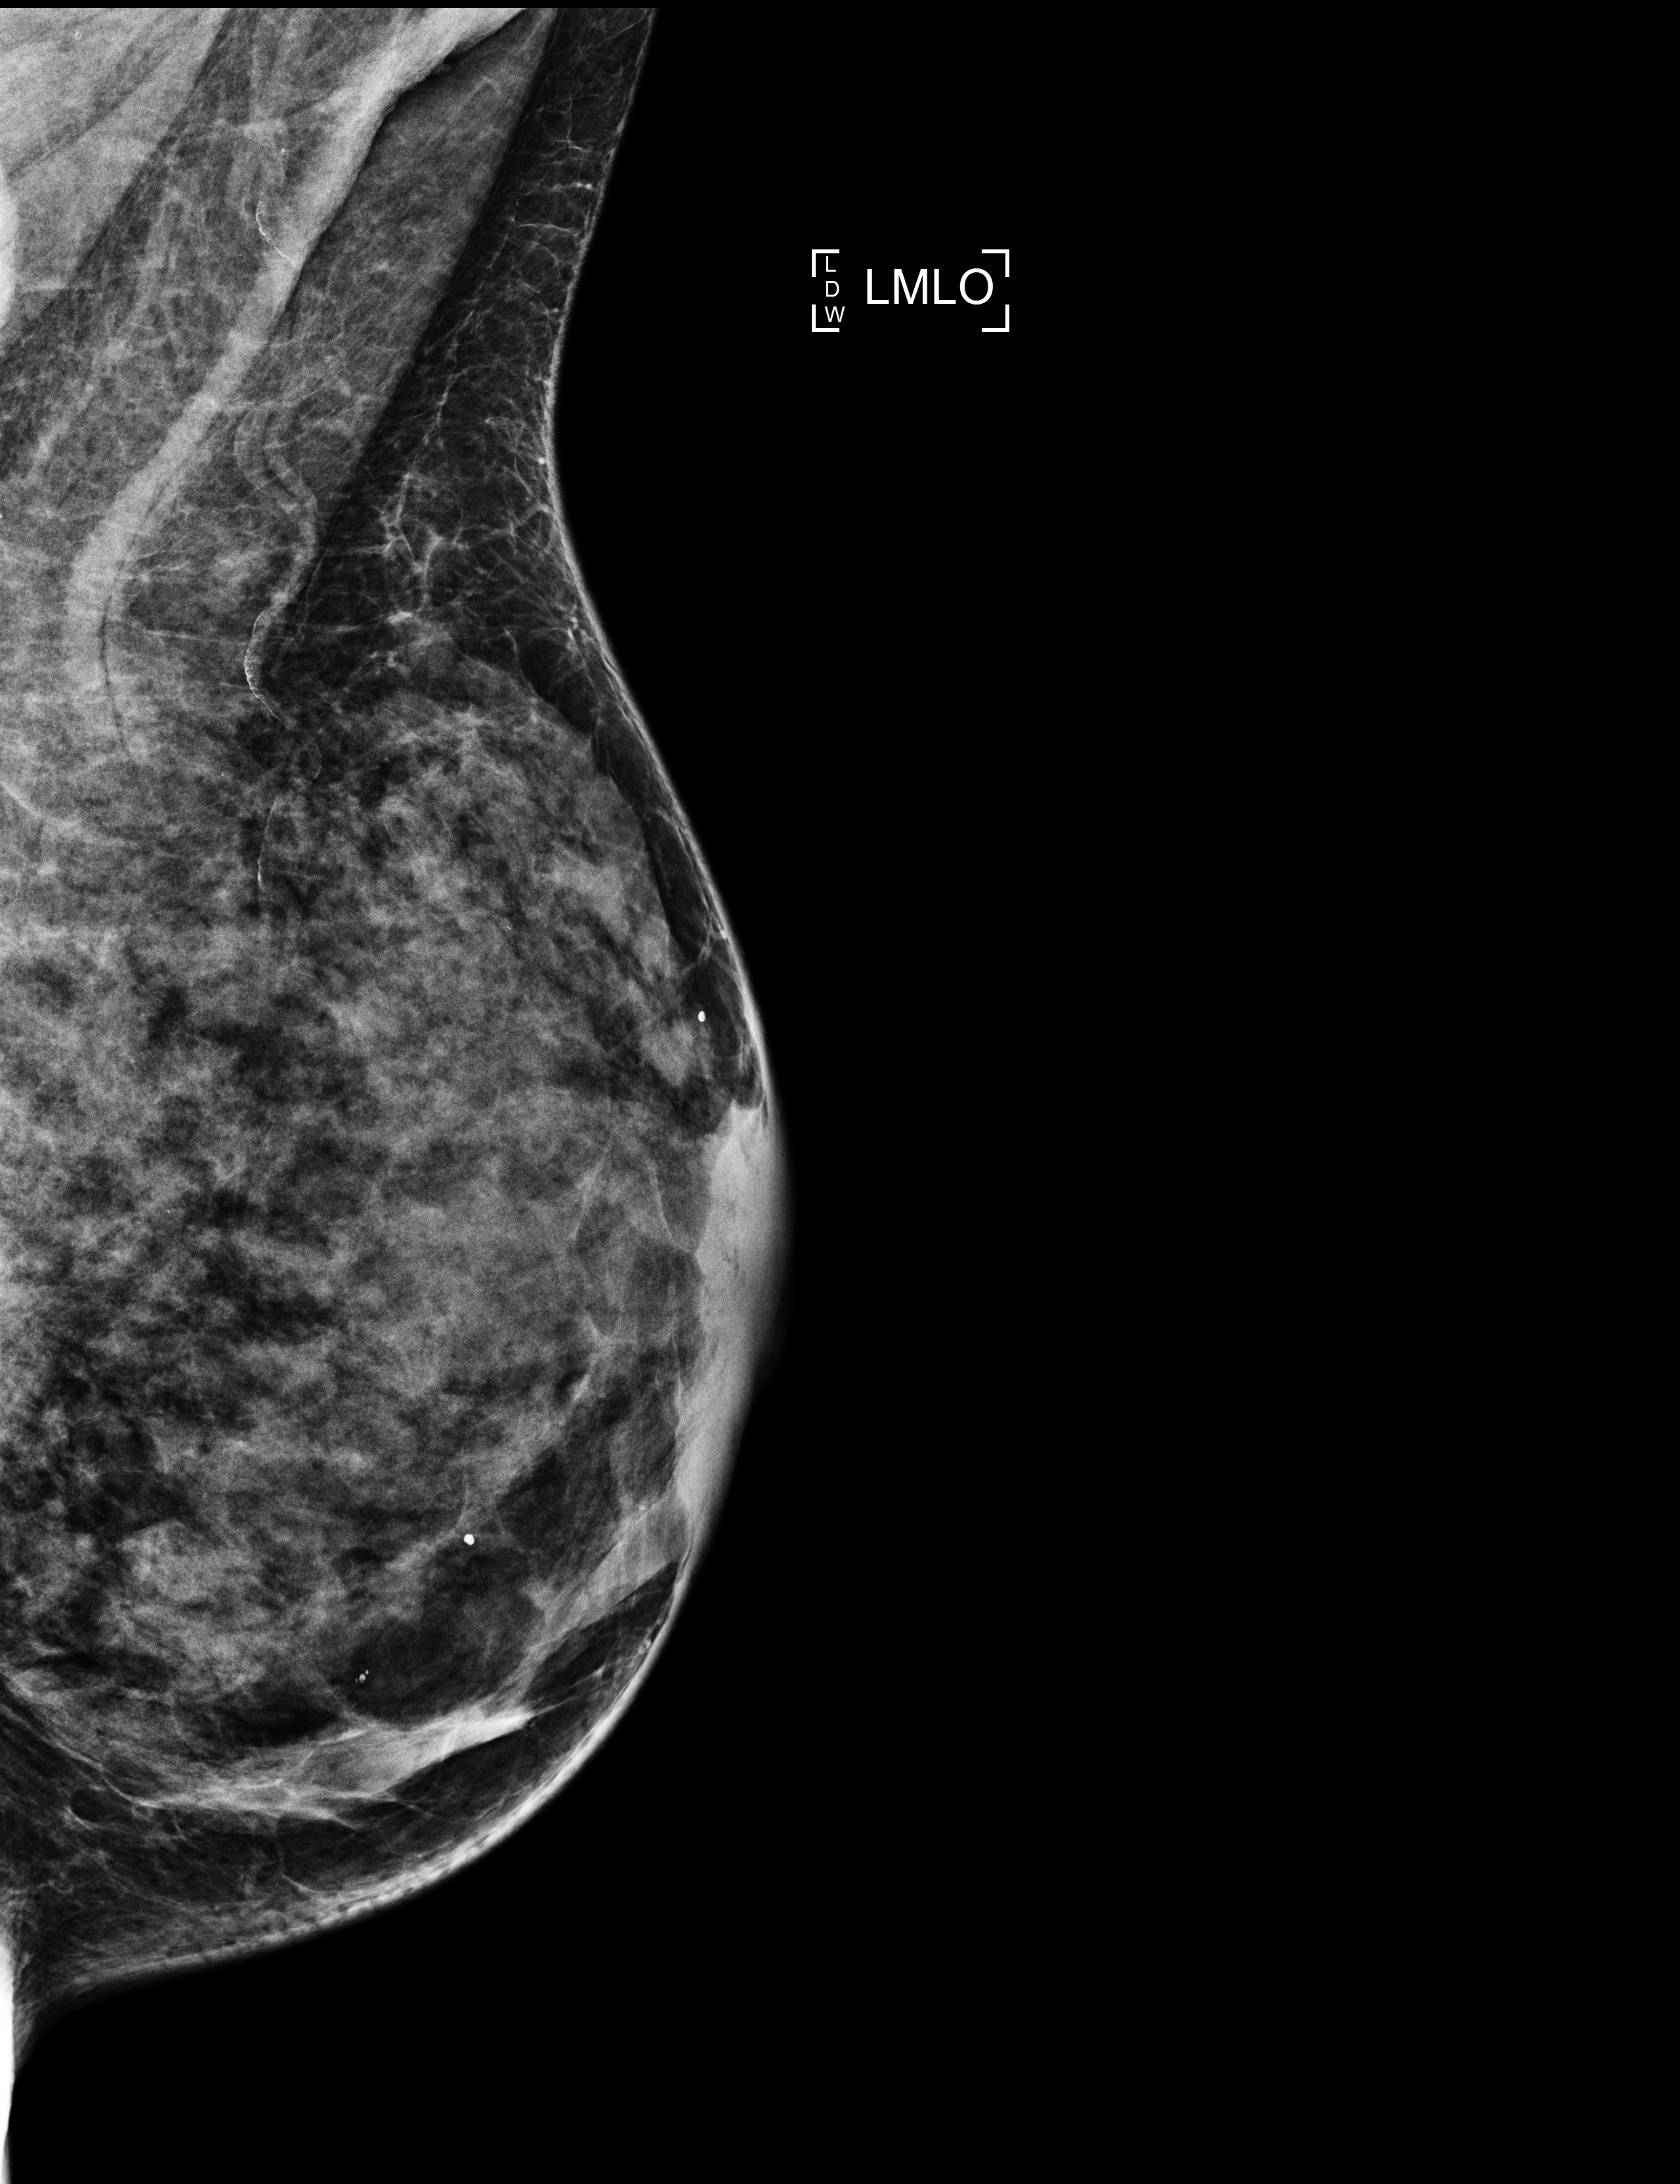
Annual screening mammography examination; system: Selenia Dimensions. Patient aged 57 years (female).
Image type: full-field digital mammogram. Breast: left. Projection: MLO view.